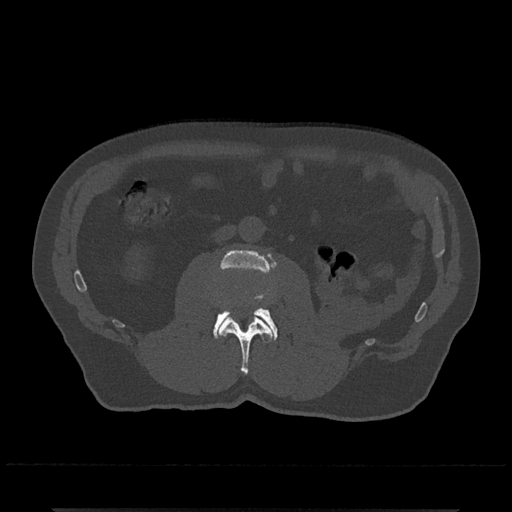
CT including the spine, one axial slice. Position 261 of 797 along the scan axis. Reconstruction kernel Br40s/3. Bone window (W 1800 / L 400 HU). 0.5 mm slice thickness. 512 × 512 image matrix, field of view 393 × 393 mm. Male patient, age 67 years. From the clinical record (not read from this slice): primary cancer: prostate.
Outlined on this slice (semi-automatically segmented with operator editing):
- L2 vertebra: bounding box <219,315,273,374> (left, top, right, bottom; pixels)
- L3 vertebra: <213,249,278,341>